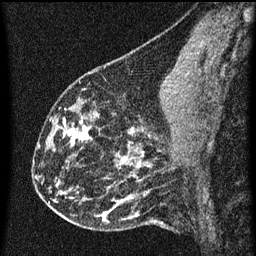
Breast MRI (dynamic contrast-enhanced), one sagittal slice; slice 25 of 60 in the series (ordered by position); dynamic contrast-enhanced series, image 2 of 3 at this slice position (ordered by acquisition); 1.5 T; TE 4.2 ms, TR 8 ms; 2 mm slice thickness; 256 × 256 image matrix, field of view 180 × 180 mm. Patient: female, 43 years.
Structures marked on this image (semi-automatic segmentation, software-assisted and operator-edited):
- analysis volume of interest (the breast-tissue region the enhancement analysis was run in; not a lesion): bounding box (x1, y1, x2, y2) in pixels: (55, 104, 102, 153)
- tumour enhancement mask (voxels above the 70 % enhancement threshold inside the analysis volume of interest): (64, 114, 97, 145)